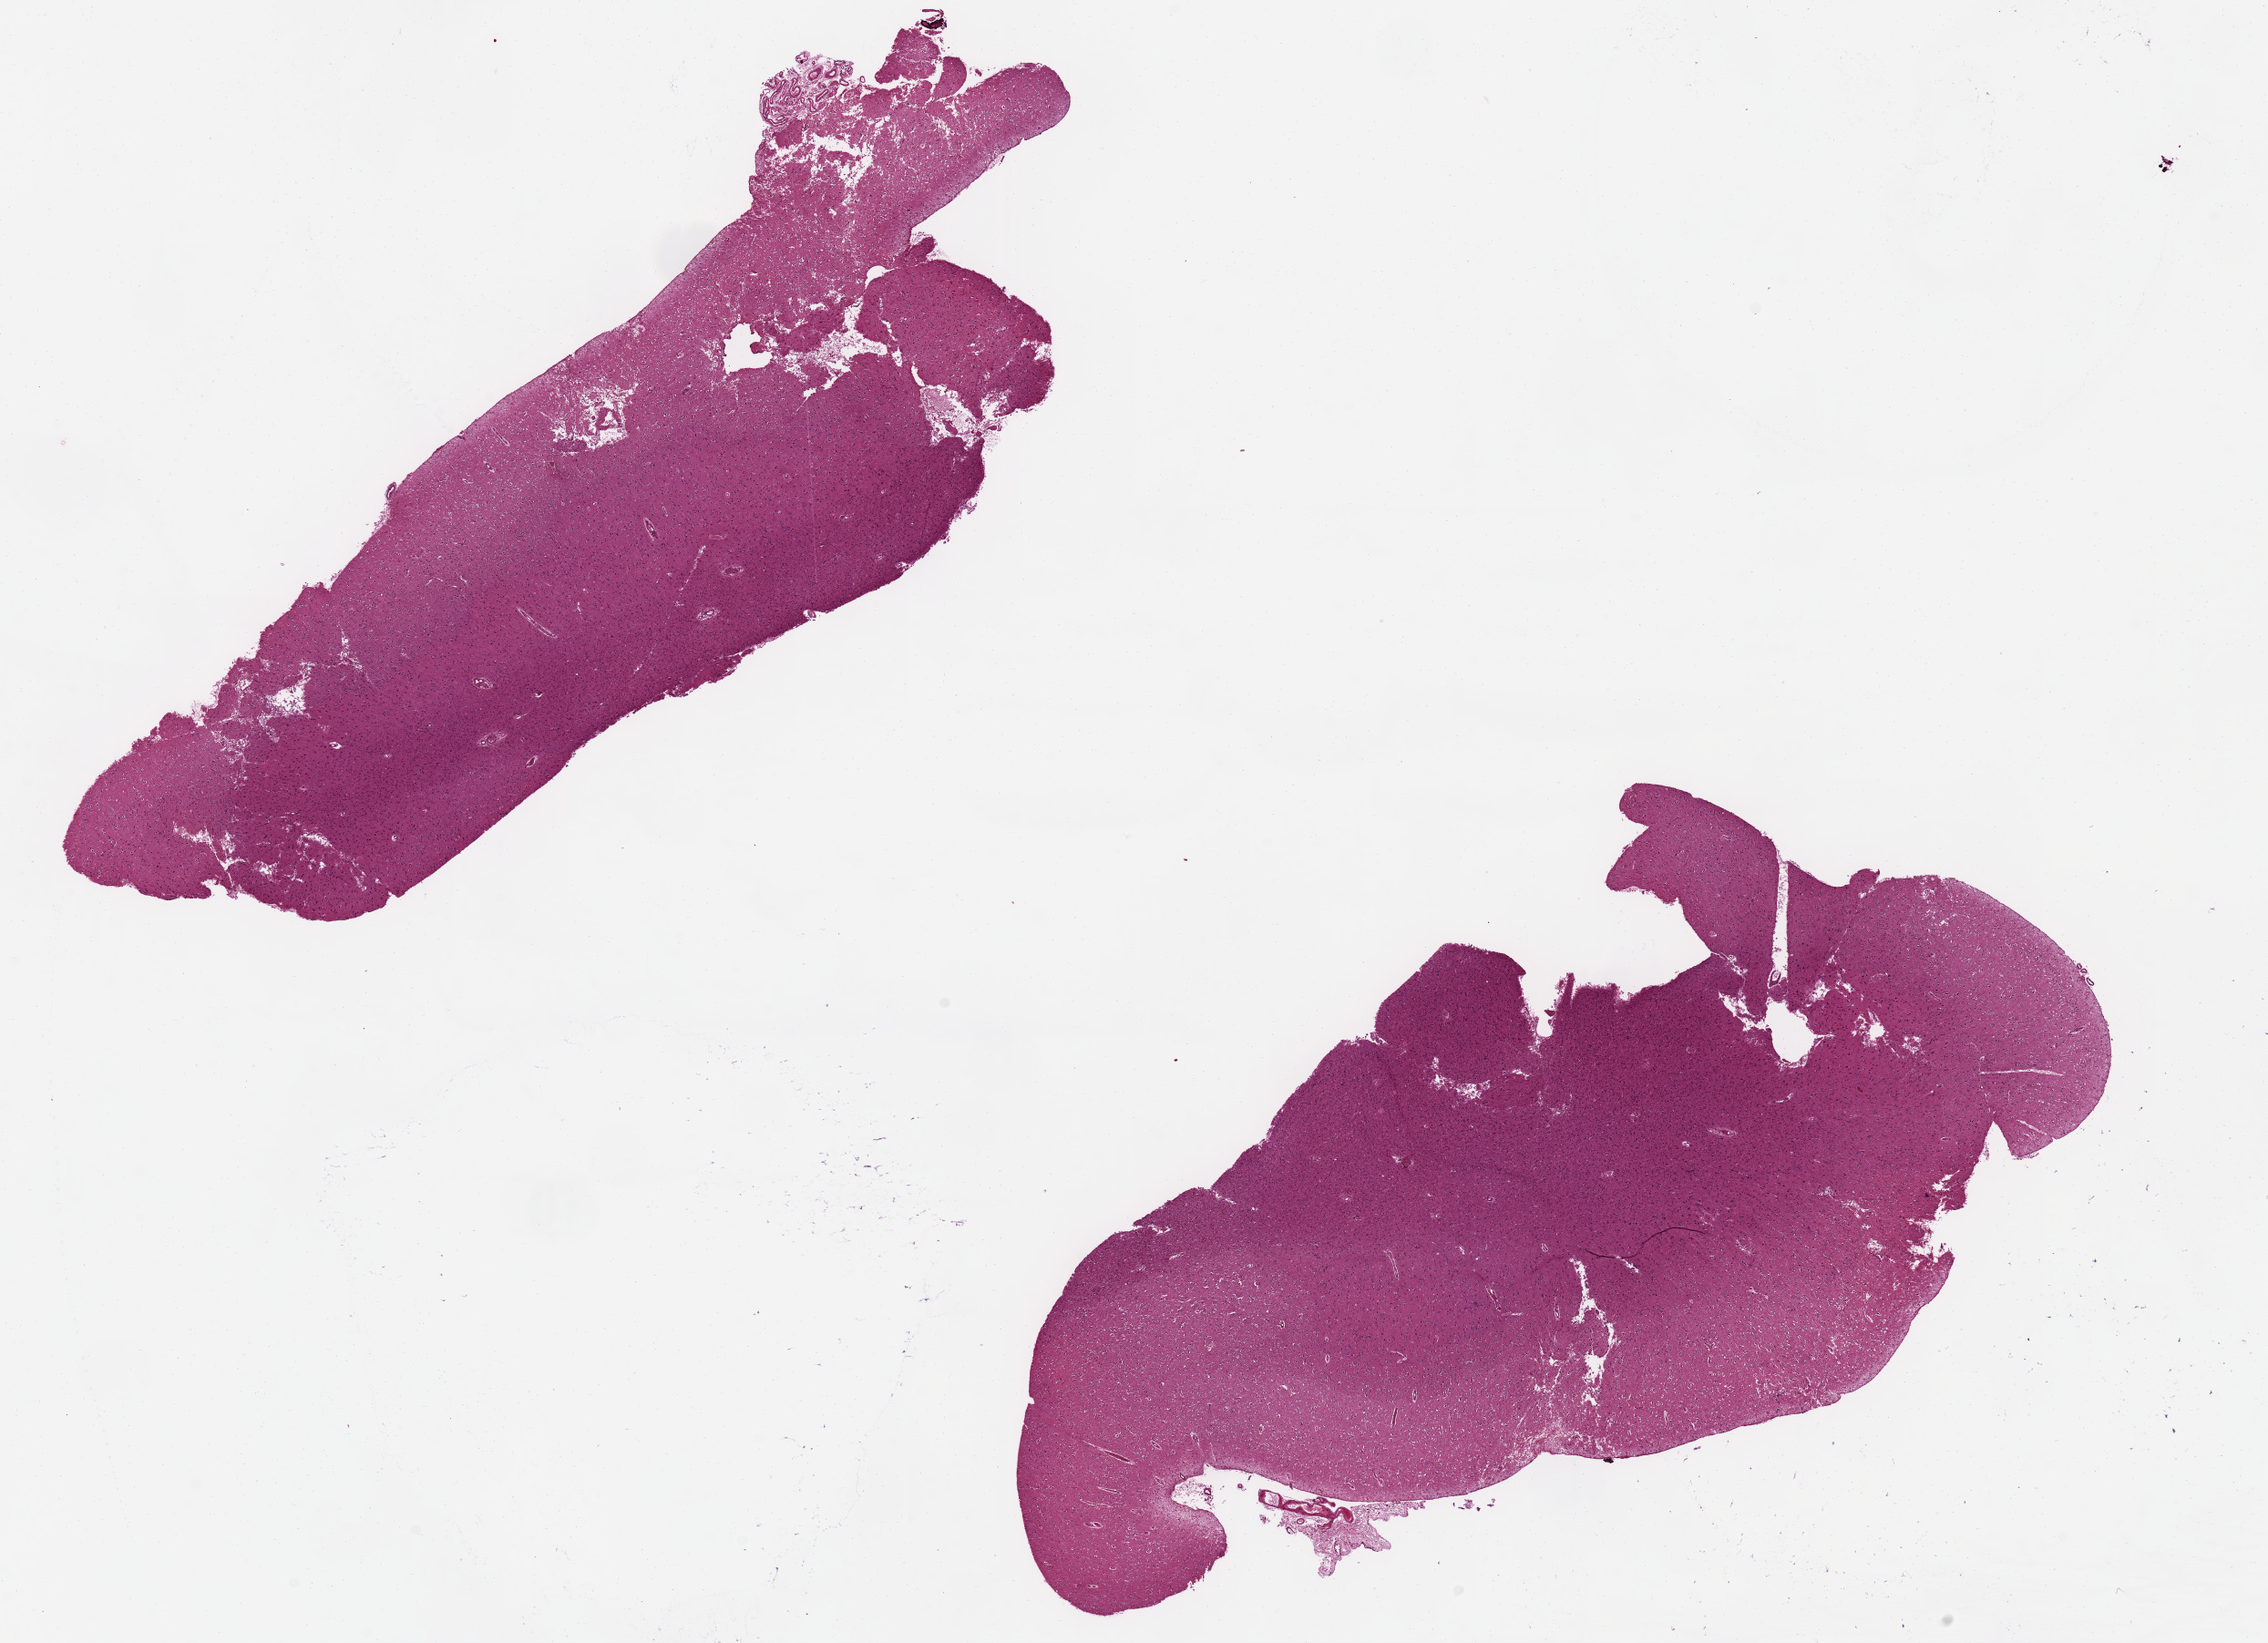
Whole-slide image, H&E stain, brightfield — whole scanned area (about 19.7 x 14.3 mm) shown as a low-resolution overview. PAXgene-fixed paraffin-embedded (PFPE) section. Sampled site (target tissue): cerebral cortex. Donor tissue sample. Female donor.
Pathologist's review note for this sample: OK for analysis.